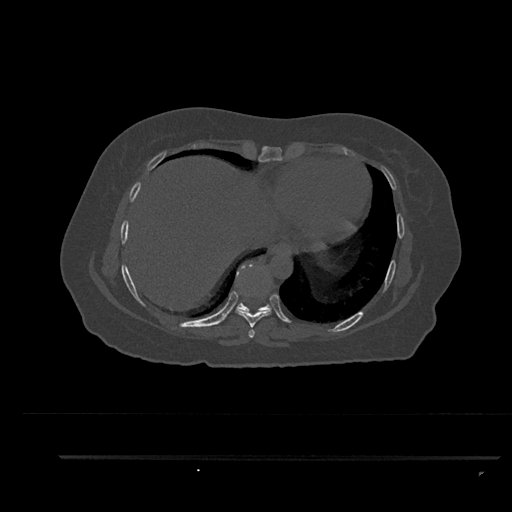
CT including the spine, one axial slice. Position 444 of 797 along the scan axis. Reconstruction kernel Br40s/3. 120 kVp. Bone window (W 1800 / L 400 HU). 0.5 mm slice thickness. 512 × 512 image matrix, field of view 408 × 408 mm. Female patient, age 44 years. From the clinical record (not read from this slice): primary cancer: renal; vertebrae with lytic lesions (as recorded): L1.
Annotated regions visible in this slice (semi-automatically segmented with operator editing):
- T7 vertebra: bounding box <248,329,255,338> (left, top, right, bottom; pixels)
- T8 vertebra: <235,293,271,328>
- T9 vertebra: <235,264,272,313>